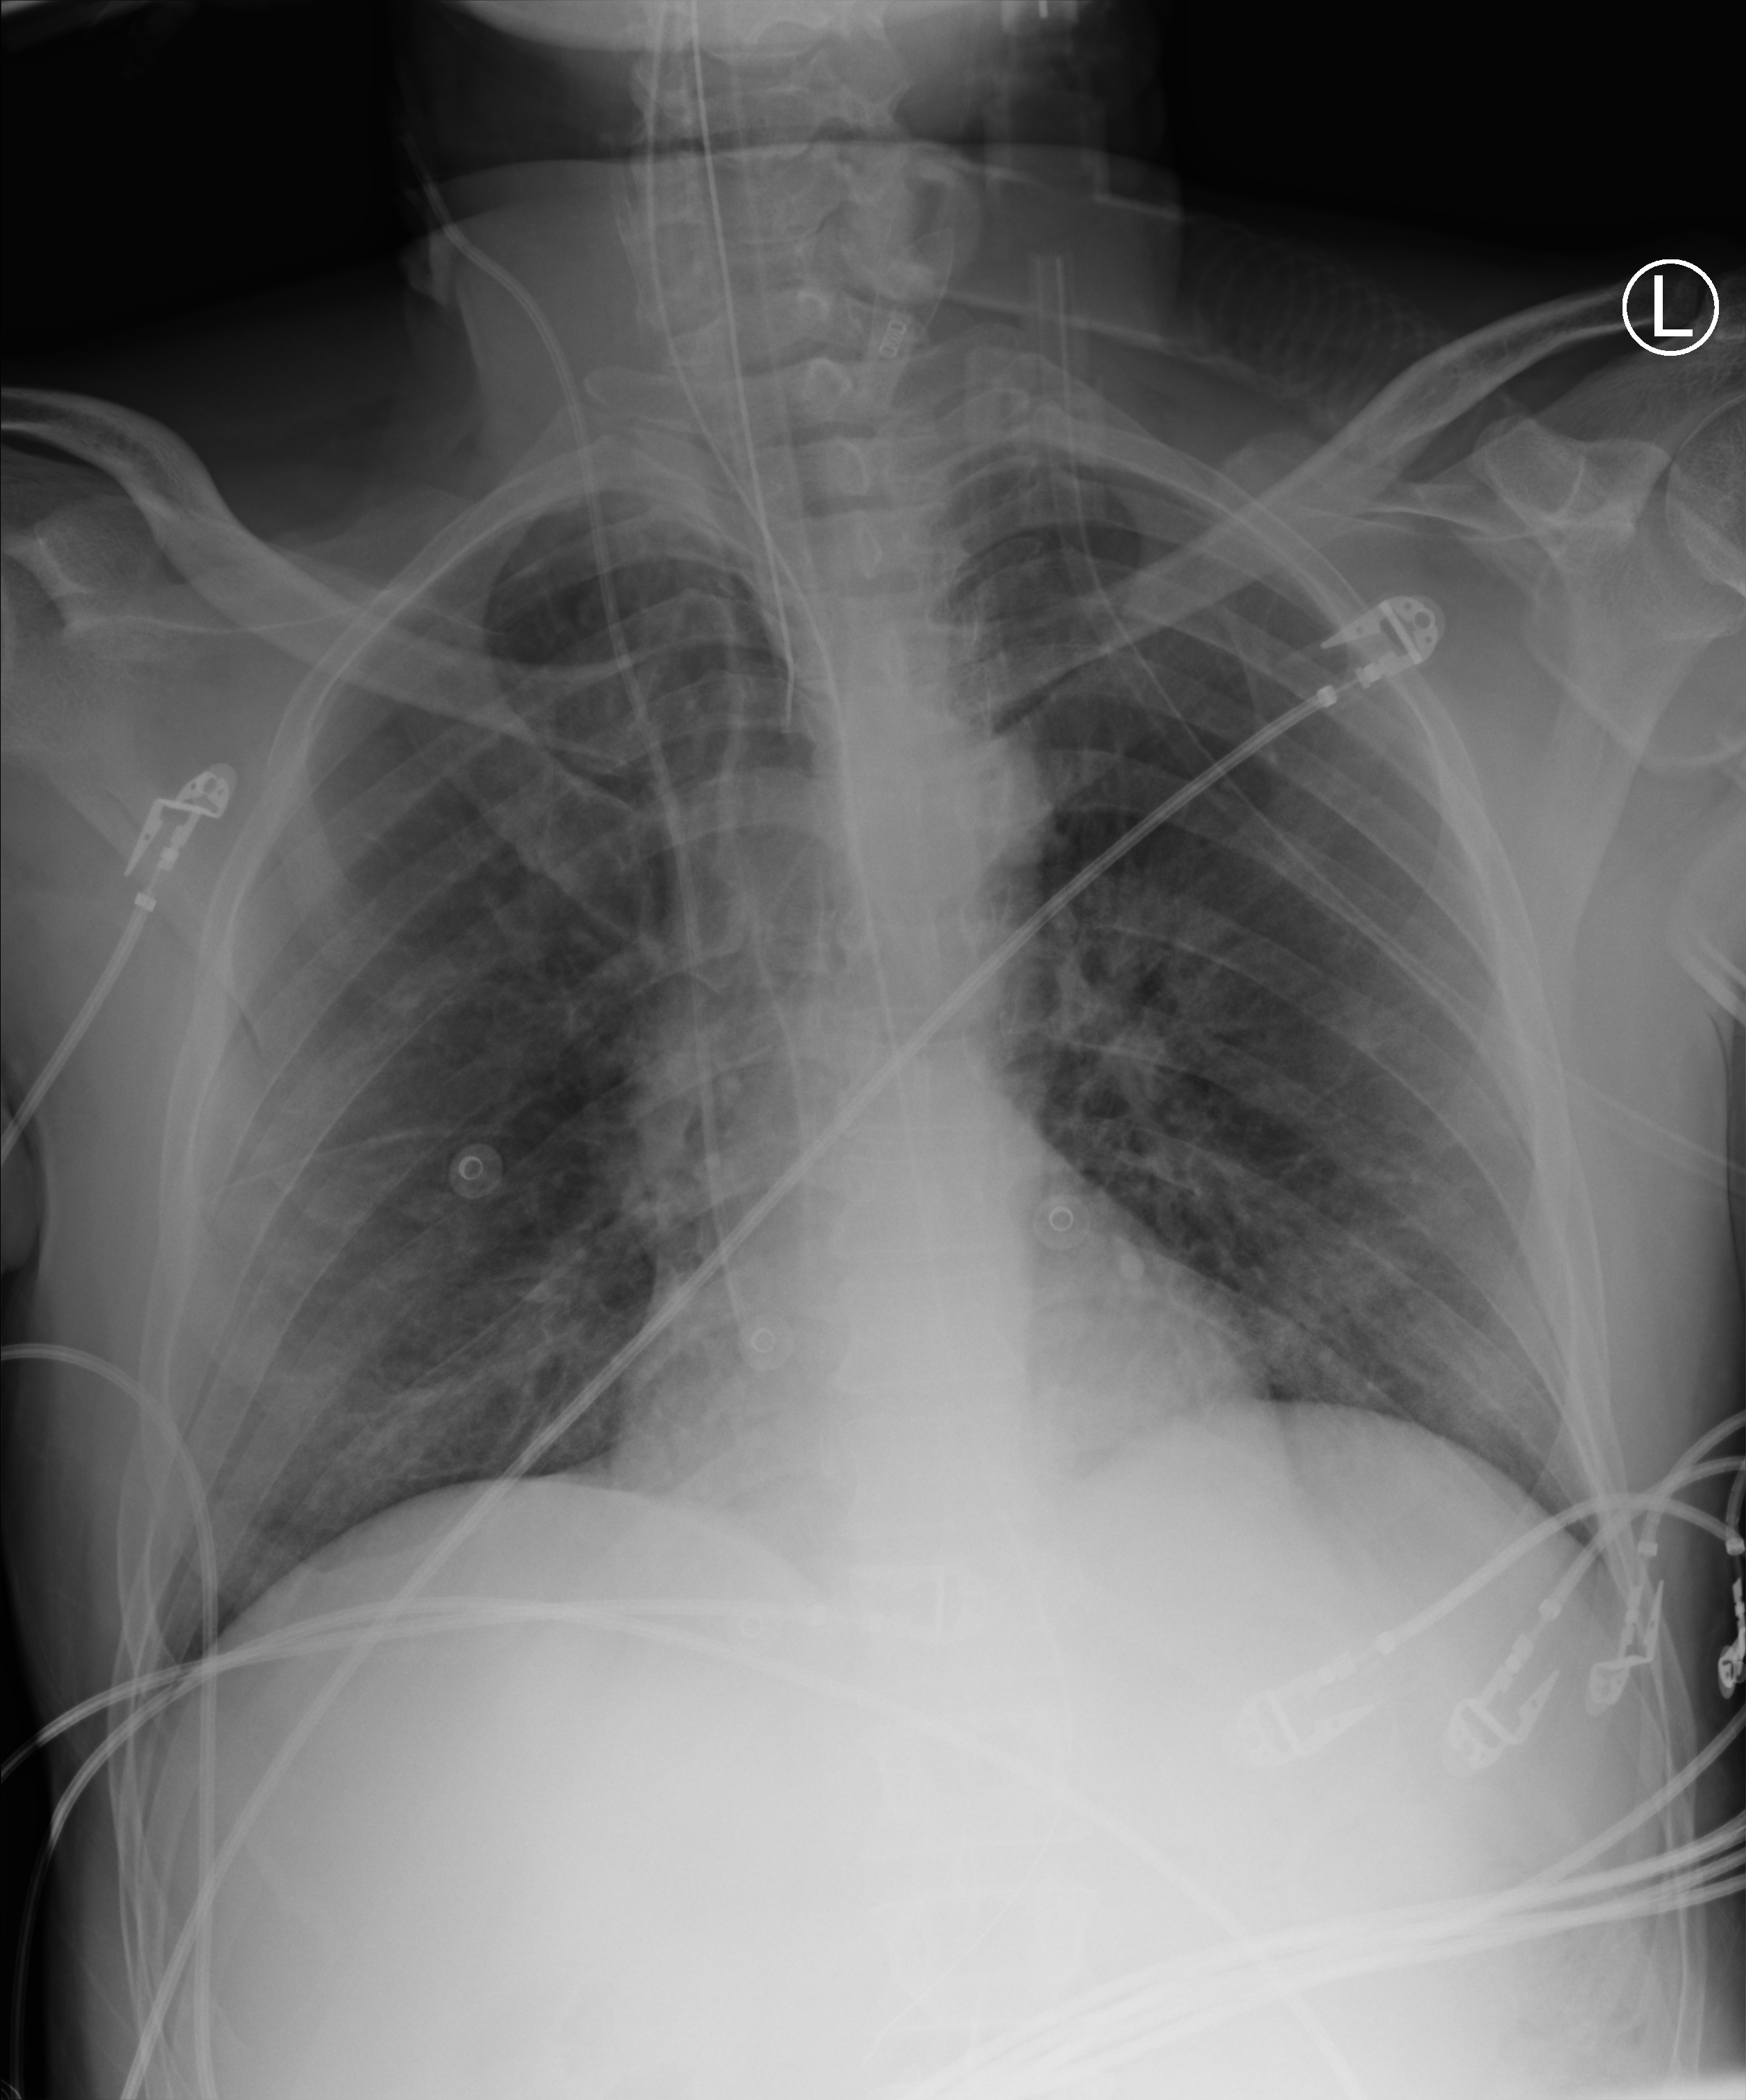
Bedside chest radiograph (computed radiography); anteroposterior (AP) projection. Patient hospitalised with COVID-19; male, aged 18–59 years.
Hospital-stay facts (about this admission, not read from this image; timing relative to this image not recorded): admitted to intensive care during this hospital stay: yes; mechanically ventilated during this hospital stay: yes; smoking status (admission record): never.